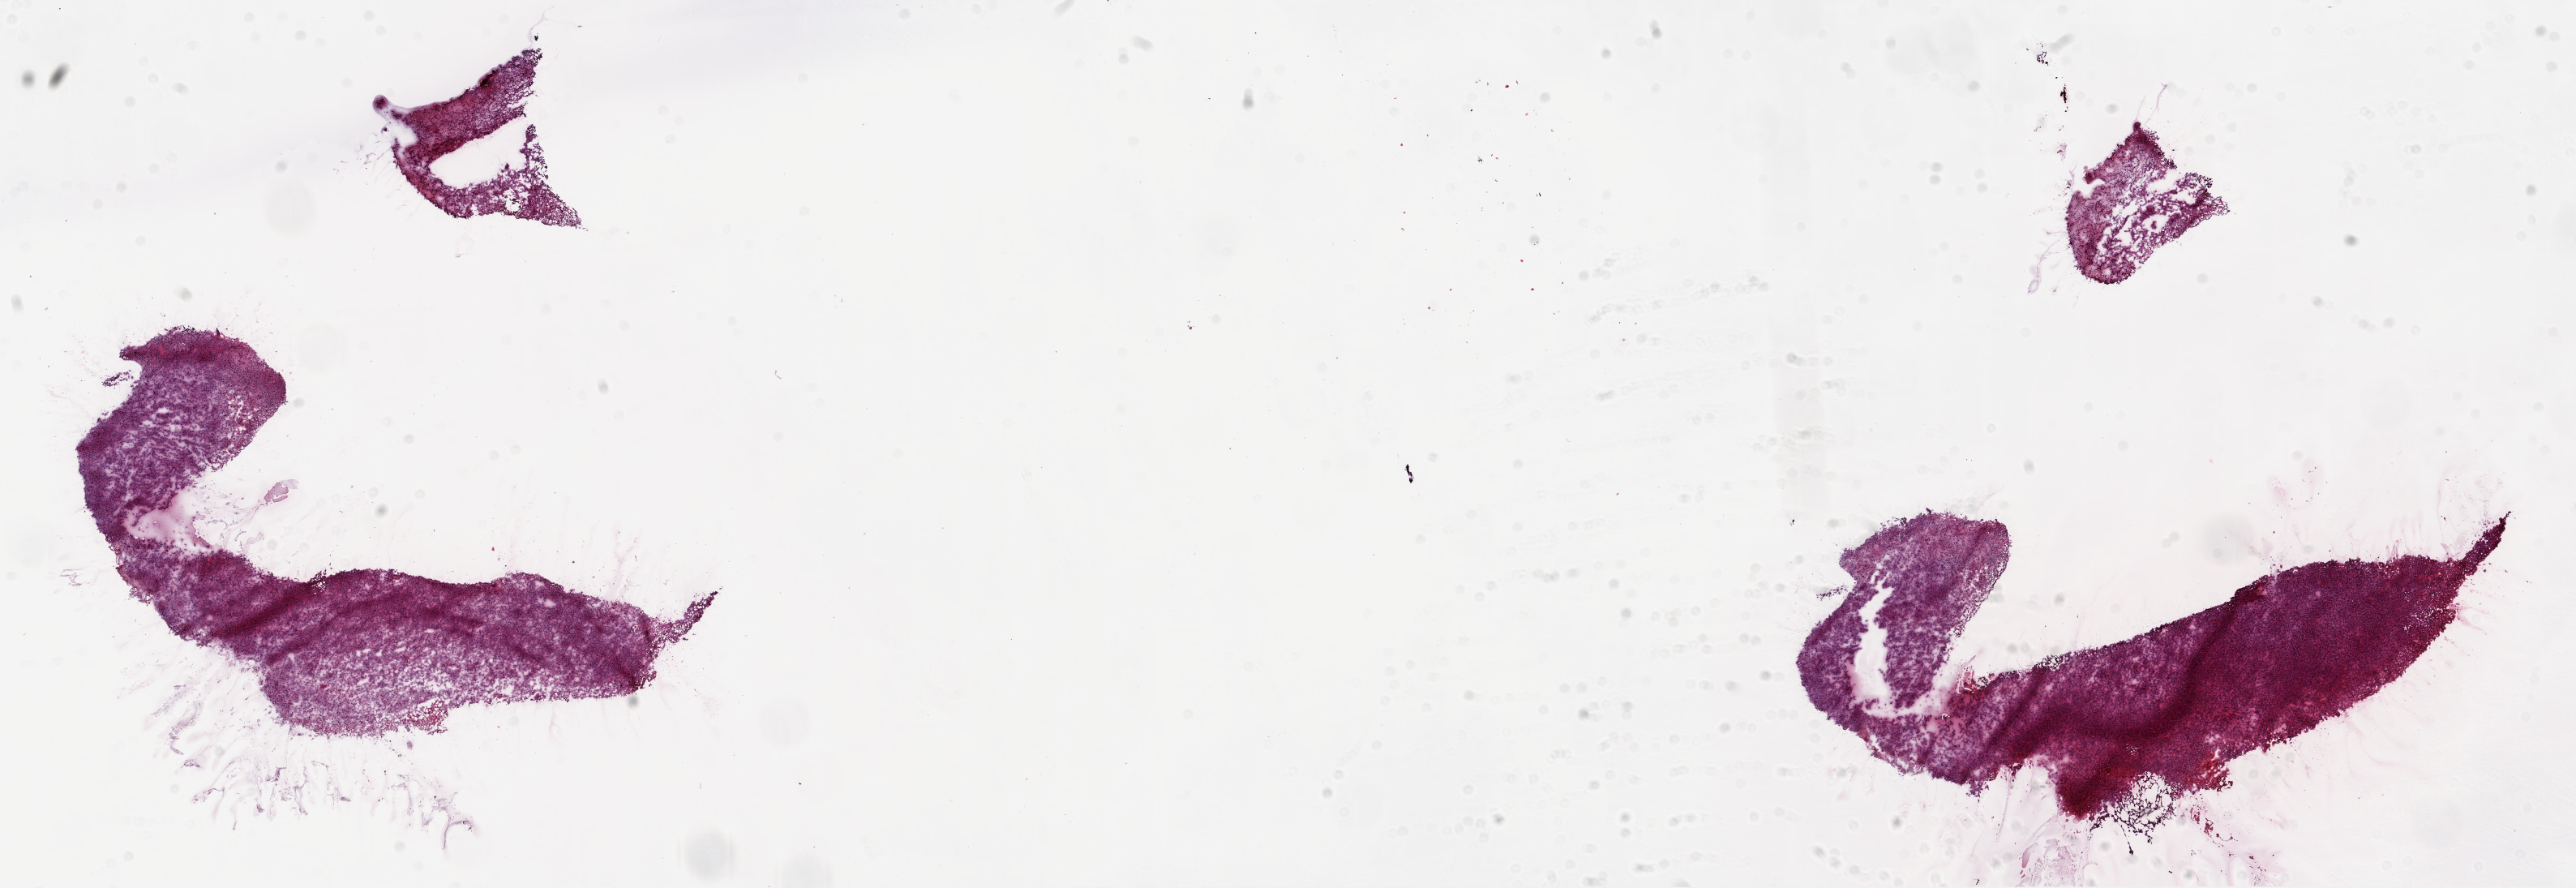
Digitized H&E-stained tissue section (whole slide), whole scanned area (about 25.6 x 8.8 mm, from a 20x scan) shown as a low-resolution overview. Frozen section. Sample: primary tumour, brain. Male patient; age at initial diagnosis 51 years. Pathologist review of this section (percent, as recorded): tumour cells 95%, tumour nuclei 100%, normal cells 0%, stromal cells 0%, necrosis 5%.
• pathologic diagnosis: Glioblastoma